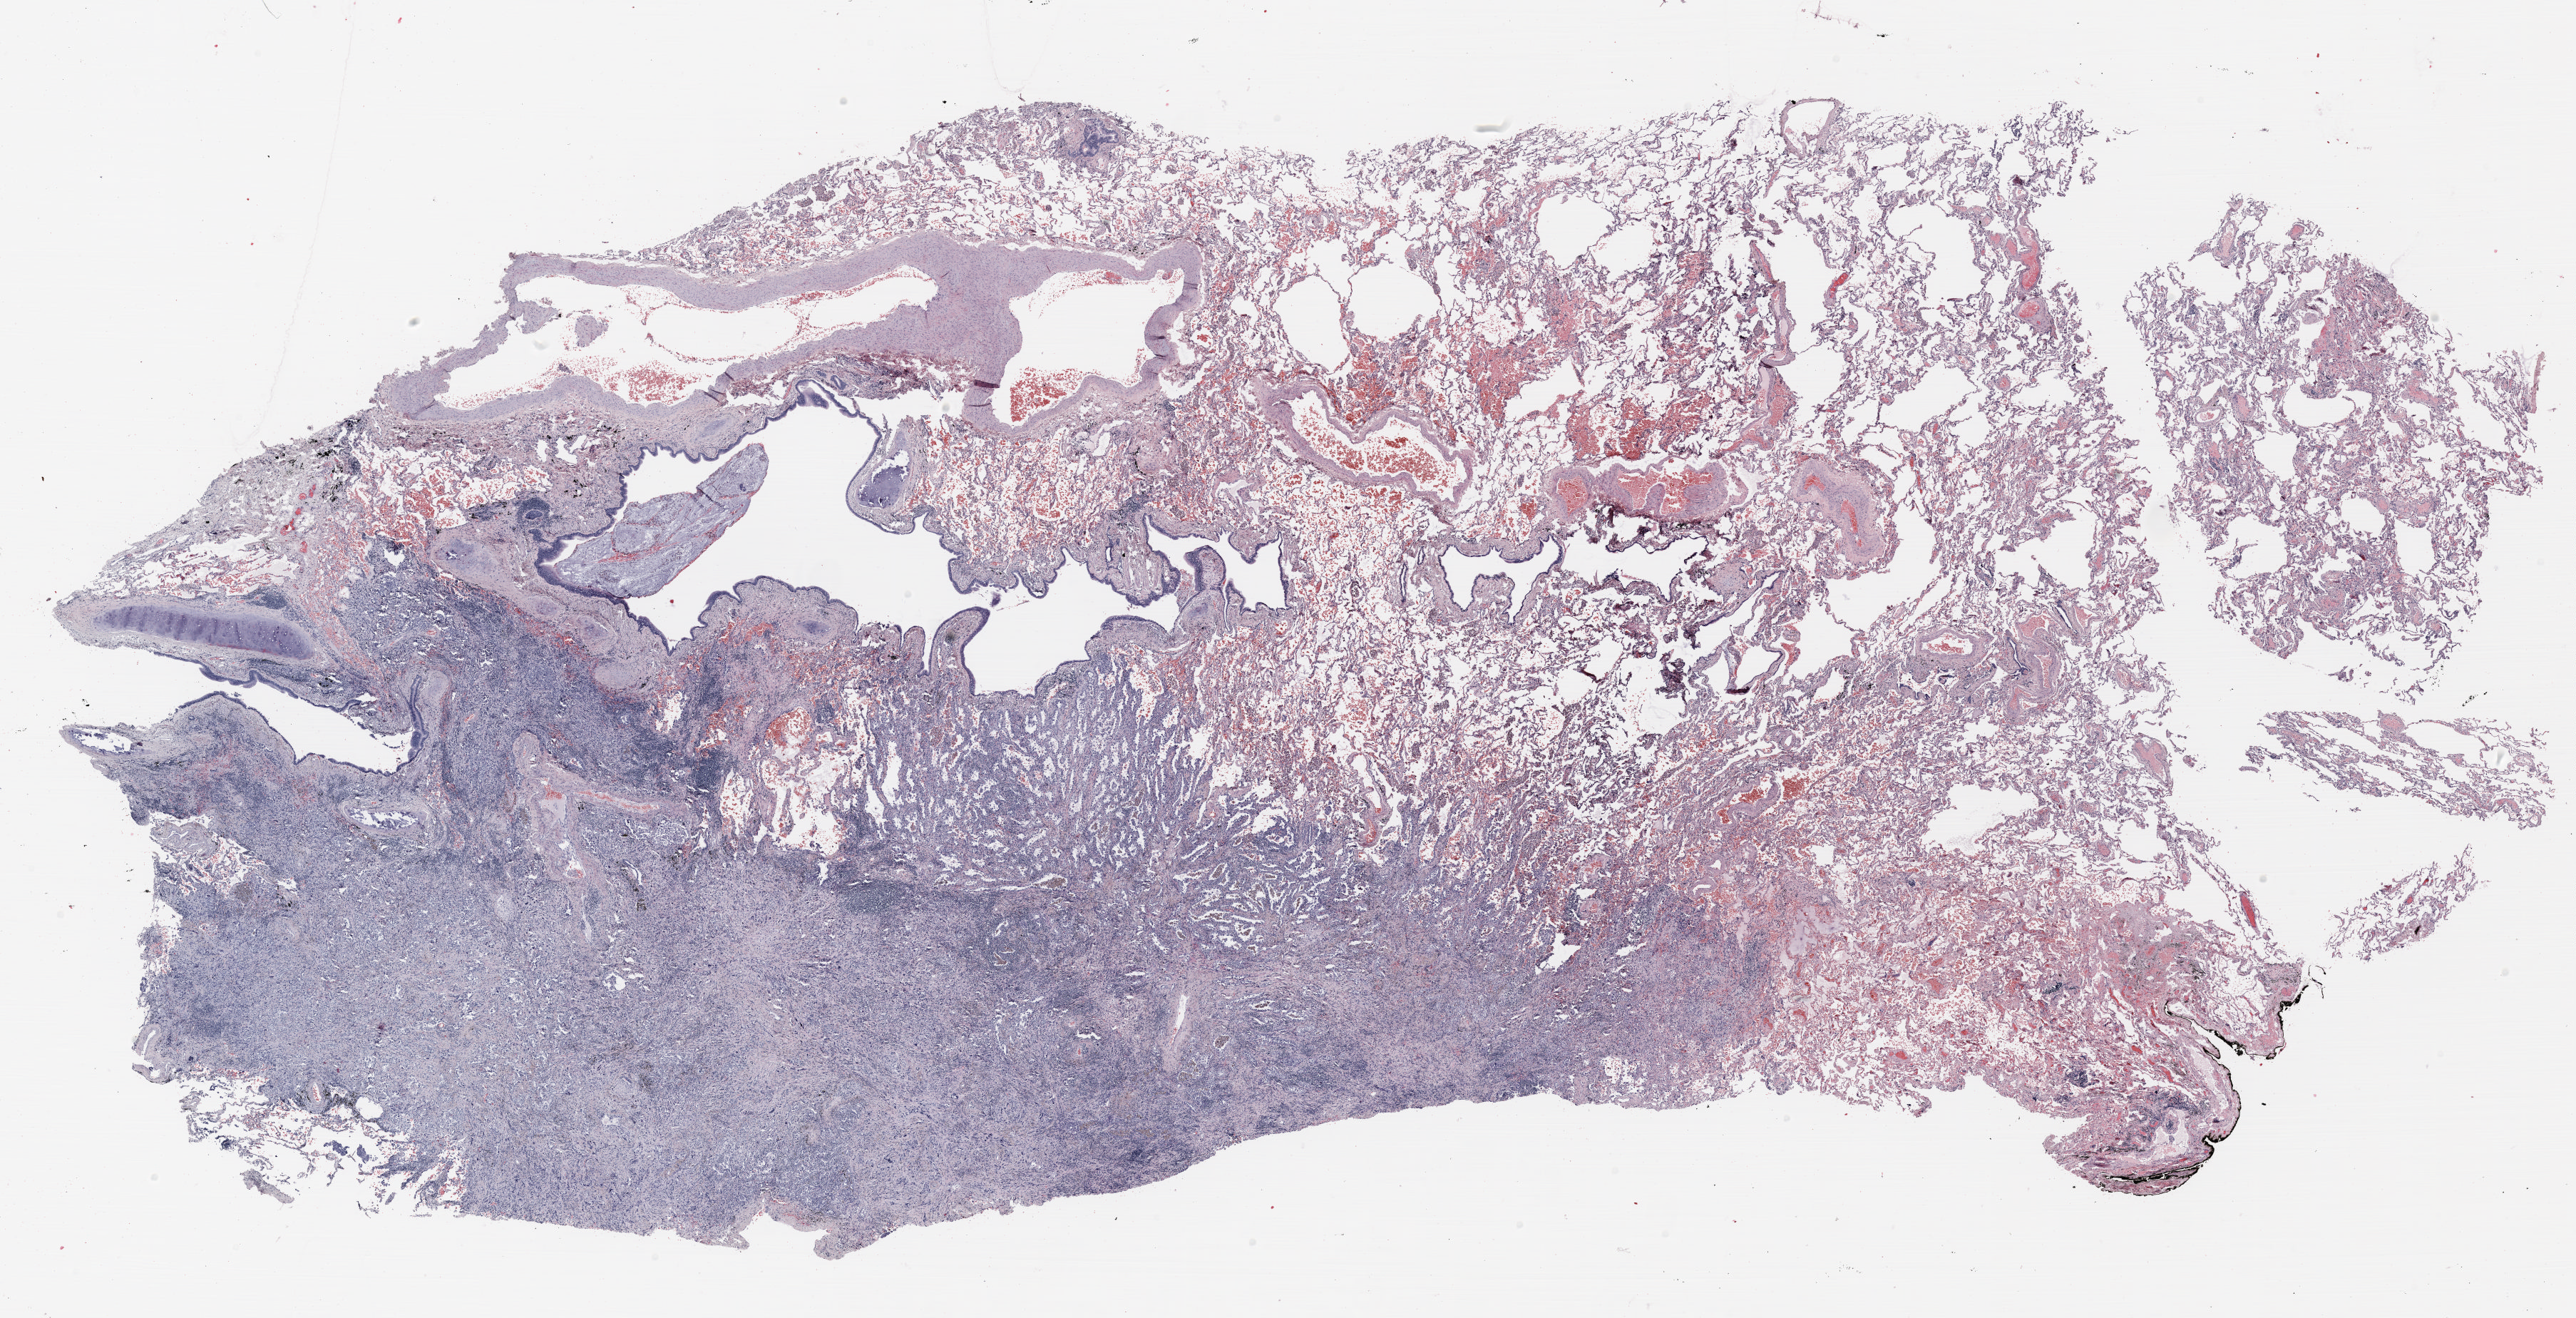
H&E whole-slide image, shown as a low-resolution overview of the whole scanned area (about 29.0 x 14.8 mm); formalin-fixed paraffin-embedded (FFPE) section; lung tissue. Male patient, aged 70 at enrolment. Current smoker at enrolment. Grade: moderately differentiated (G2).
Stage (AJCC 6th edition): IIIA. ICD-O-3 topography: upper lobe of lung (C34.1). Tumour size (pathology): 17 mm. Participant's lung-cancer diagnosis: Adenocarcinoma, NOS (ICD-O-3 8140/3). Primary tumour location (clinical record): left upper lobe.